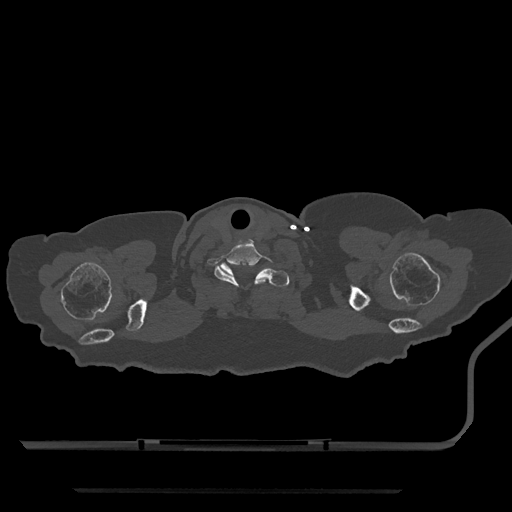
CT including the spine, one axial slice; slice 729 of 797 in the series (ordered by position); bone window (W 1800 / L 400 HU); 0.5 mm slice thickness; 512 × 512 image matrix. Female patient, age 51 years. From the clinical record (not read from this slice): primary cancer: neuro; vertebrae with lytic lesions (as recorded): T8.
Outlined on this slice (semi-automatic segmentation, software-assisted and operator-edited):
- T1 vertebra: bounding box <220,263,290,287> (left, top, right, bottom; pixels)